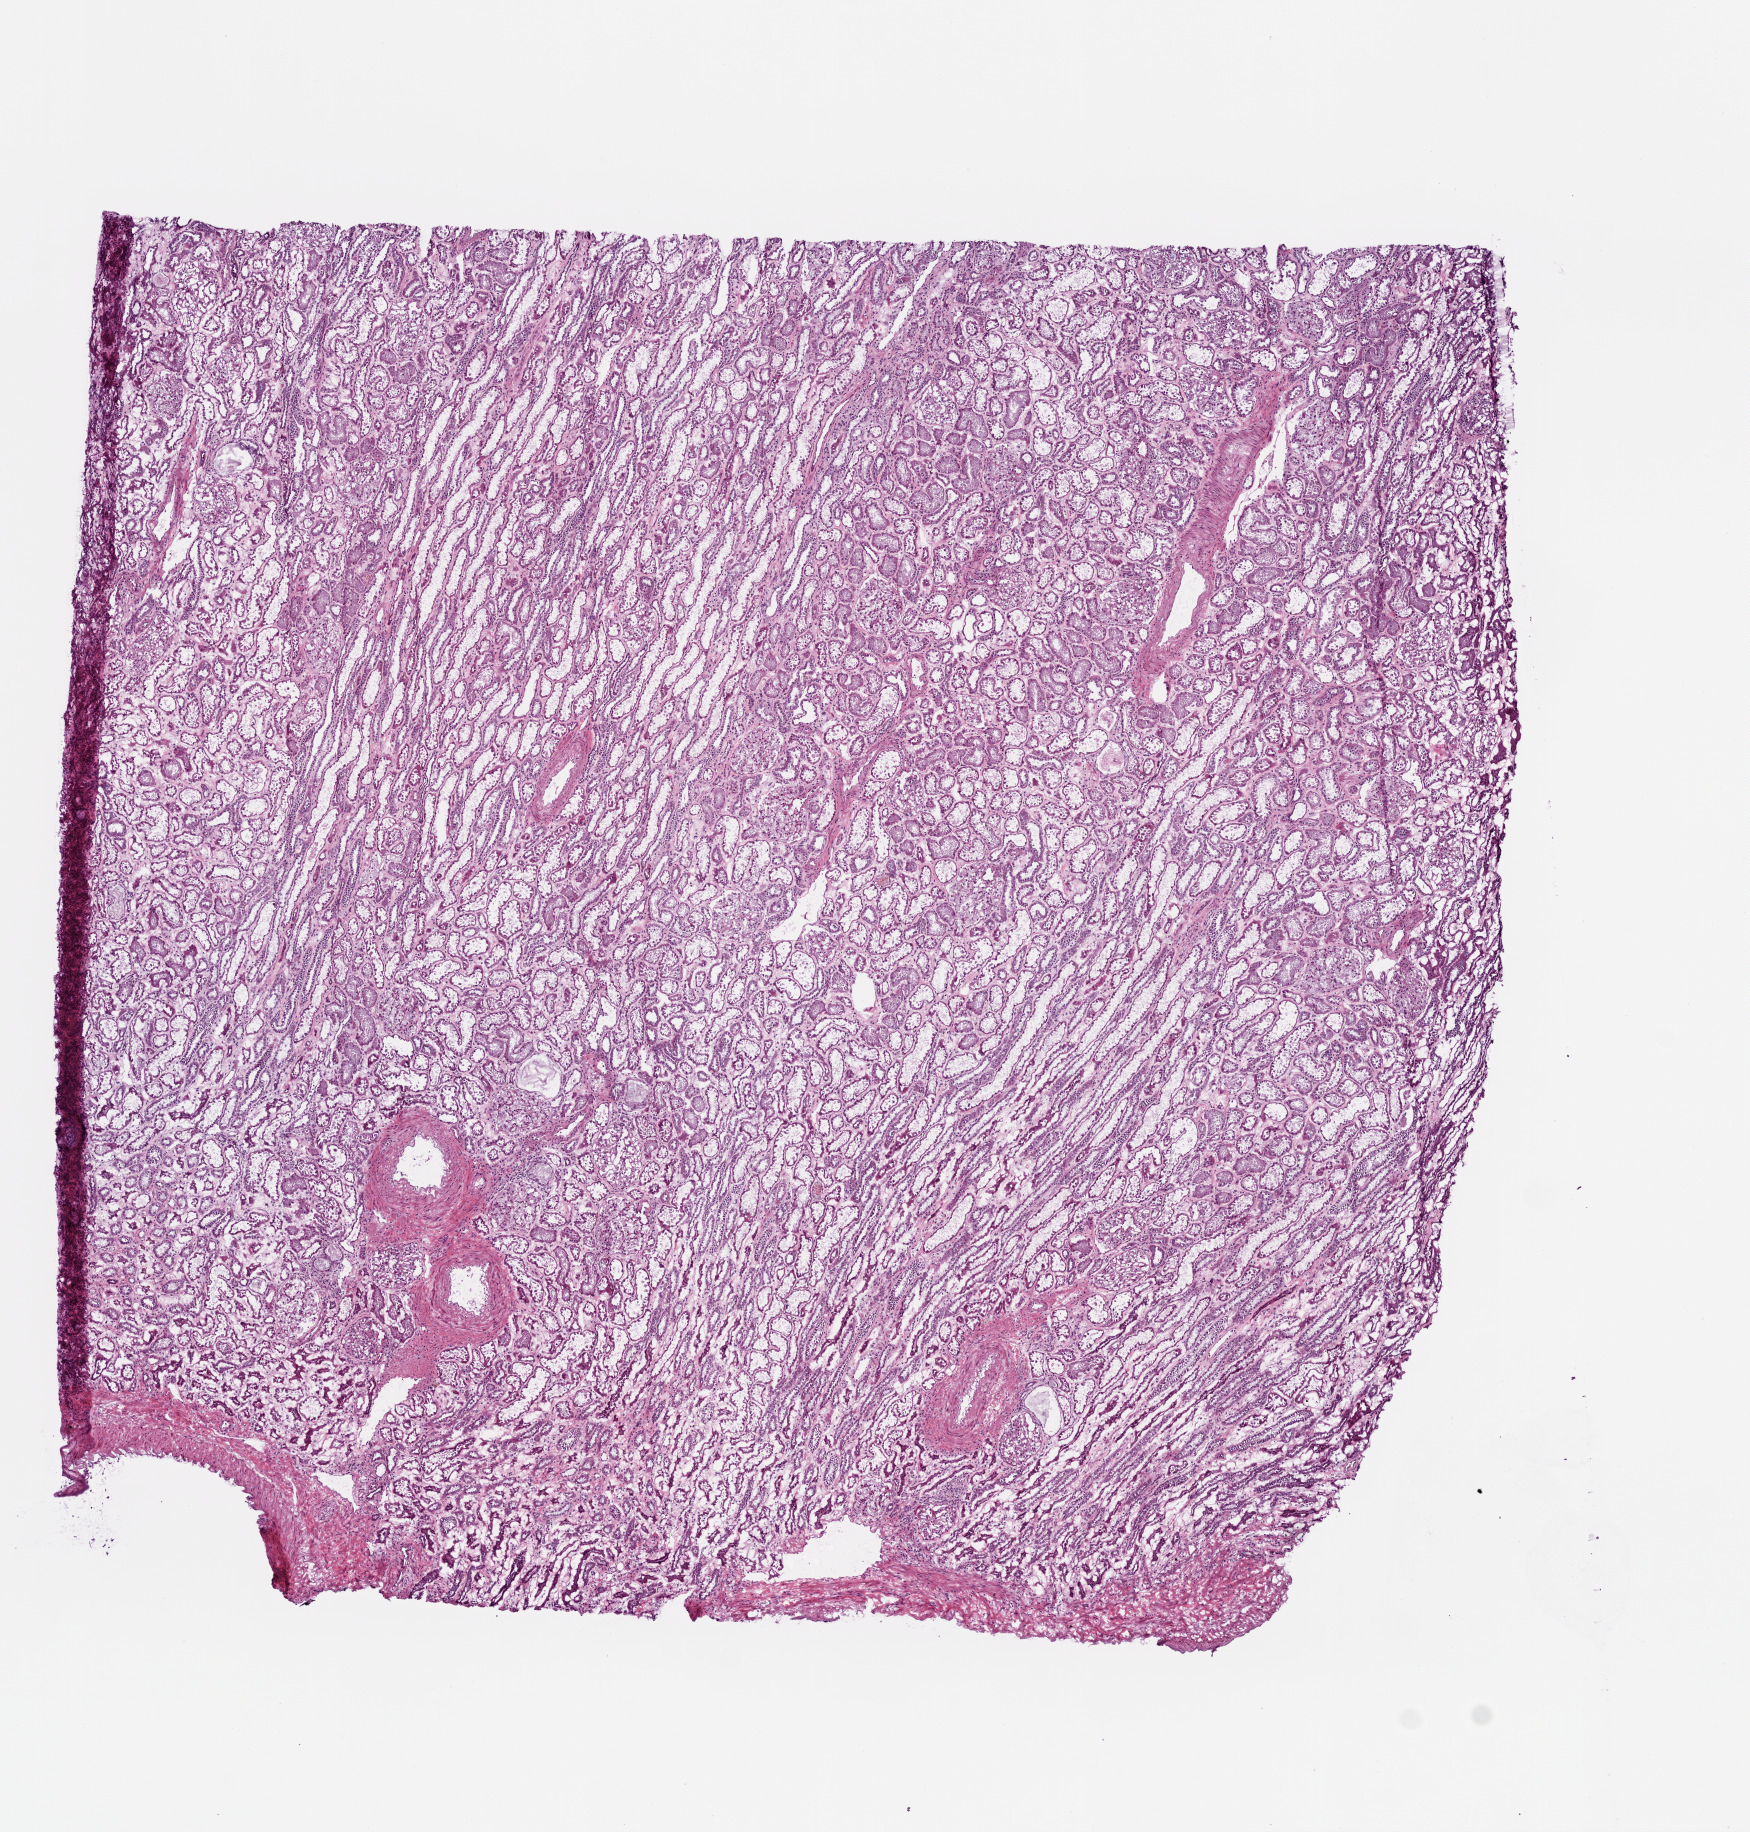
Whole-slide histology image, H&E, a low-resolution overview of the entire scanned area, about 7.0 x 7.3 mm. Frozen section from the top of the tissue portion. Solid tissue normal (non-tumour tissue) sample from the kidney. Male, age 51 years at initial diagnosis.
* this section: solid tissue normal sample (biorepository sample class)
* patient diagnosis: Clear cell adenocarcinoma, NOS